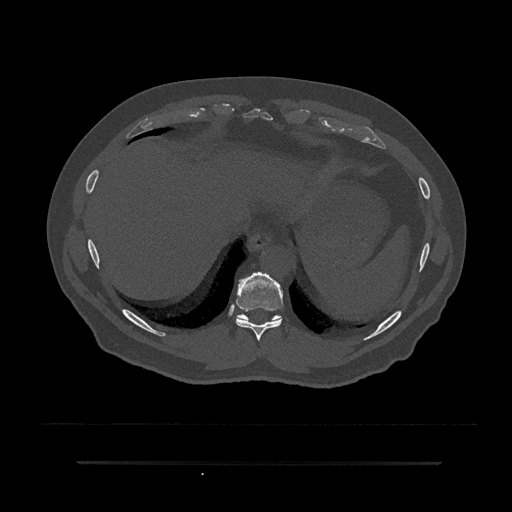
CT including the spine, one axial slice; position 363 of 797 along the scan axis; reconstruction kernel Br40s/3; bone window (W 1800 / L 400 HU); 0.5 mm slice thickness; 512 × 512 image matrix. Patient: male, 59 years. Case-level facts recorded for this patient, not image findings: primary cancer: bile ducts.
Structures marked on this image (semi-automatic segmentation, software-assisted and operator-edited):
- T10 vertebra: bounding box [x1, y1, x2, y2] px = [237, 314, 280, 327]
- T9 vertebra: [236, 272, 284, 341]